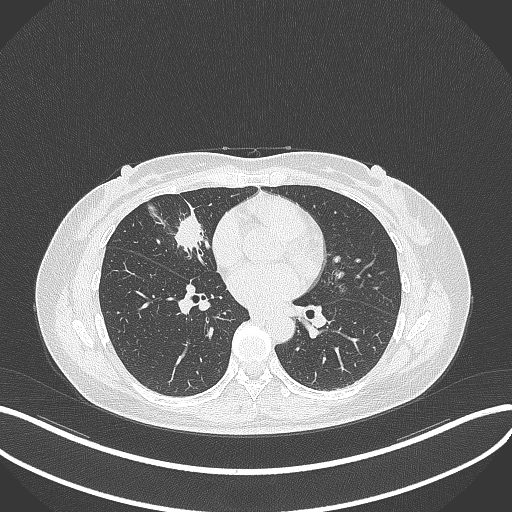
Chest CT, one axial slice; position 137 of 284 along the scan axis; lung window (W 1500 / L -600 HU); 1 mm slice thickness; 512 × 512 image matrix, field of view 400 × 400 mm. Patient: female, 43 years. From the clinical record (not read from this slice): clinical TNM (as recorded): T1c N3 M1; histopathological grade: G1.
Annotated regions visible in this slice (bounding box drawn by a radiologist):
- lung tumour (recorded histology: adenocarcinoma): bounding box [x1, y1, x2, y2] px = [171, 208, 215, 259]